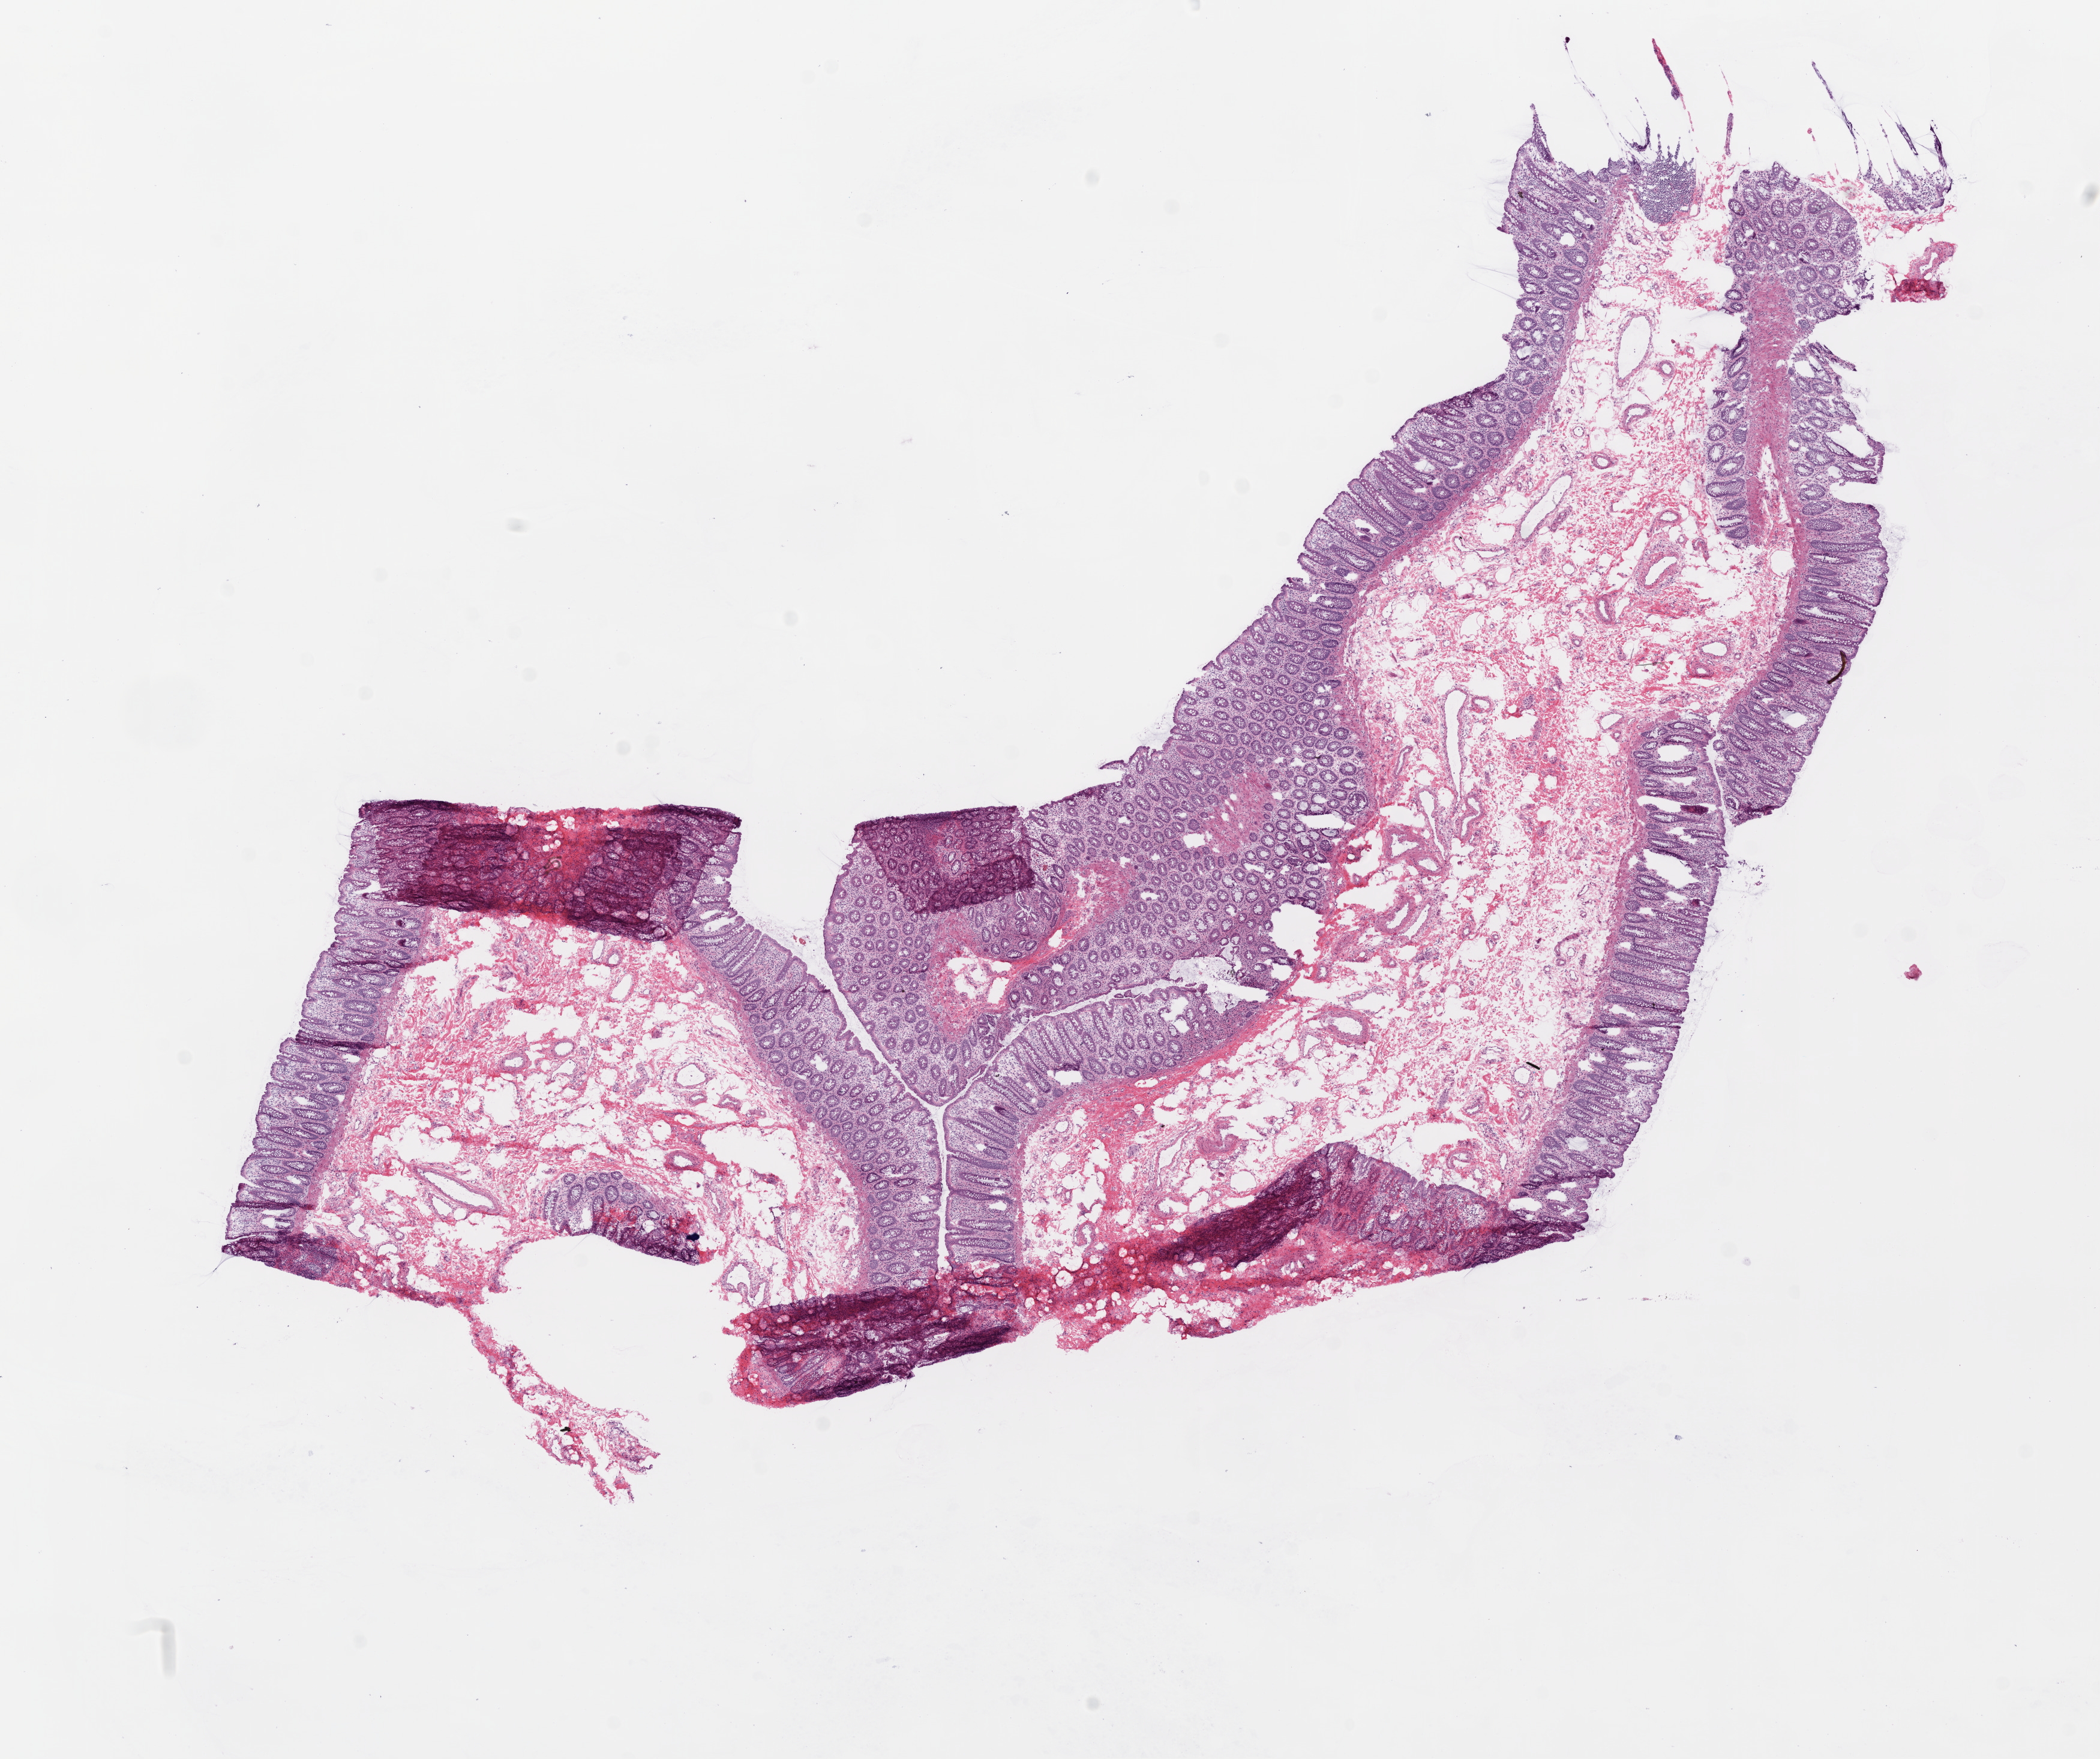
Whole-slide histology image, H&E-stained — a low-resolution overview of the entire scanned area, about 14.0 x 11.8 mm (slide scanned at 20x); frozen section from the top of the tissue portion; solid tissue normal (non-tumour tissue) sample from the rectum. Patient: male, age at initial diagnosis 60 years.
This section: solid tissue normal sample (biorepository sample class). Patient diagnosis: Adenocarcinoma, NOS (rectosigmoid junction).